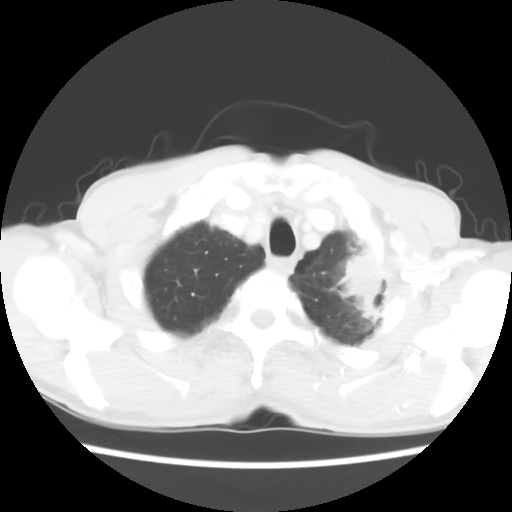
Chest CT, one axial slice. Reconstruction kernel STANDARD. 120 kVp. Lung window (W 1500 / L -600 HU). 512 × 512 image matrix, field of view 308 × 308 mm. Male patient, age 64 years. From the clinical record (not read from this slice): clinical TNM (as recorded): T3 N3 M0; histopathological grade: G3.
Outlined on this slice (rectangle marked by the reading radiologist):
- lung tumour (recorded histology: adenocarcinoma): bounding box (x1, y1, x2, y2) in pixels: (328, 244, 389, 331)